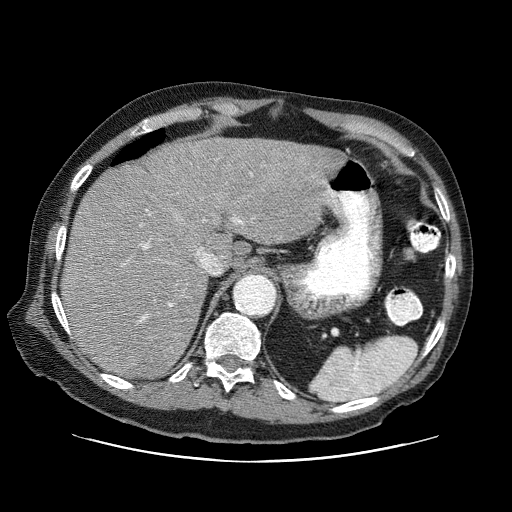
Contrast-enhanced abdominal CT (liver protocol), one axial slice. Position 54 of 87 along the scan axis. Reconstruction kernel STANDARD. 120 kVp. One of 3 acquisitions stored at this slice position. Soft-tissue window (W 400 / L 40 HU). 2.5 mm slice thickness. 512 × 512 image matrix. Case-level facts recorded for this patient, not image findings: diagnosis: hepatocellular carcinoma (patient treated with transarterial chemoembolisation; whether this scan precedes or follows treatment is not stated here); TNM stage (as recorded): Stage-IIIA; Child-Pugh class: A.
Annotated regions visible in this slice (semi-automatically segmented with operator editing):
- abdominal aorta: box from (x=236, y=274) to (x=274, y=315) px
- liver parenchyma outside the tumour (the mass and vessels are separate outlines, so this box may not span the whole liver): (x=60, y=138)–(x=344, y=378)
- liver vessels: (x=140, y=173)–(x=253, y=321)